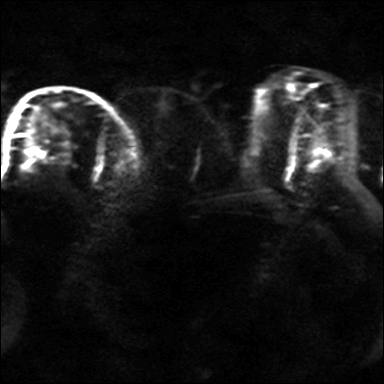
Breast MRI, one axial slice. Slice 20 of 36 in the series (ordered by position). Diffusion-weighted series; image 2 of 4 stored at this slice position (different b-values; order by instance number). 3 T. 4 mm slice thickness. 384 × 384 image matrix, field of view 320 × 320 mm. Female patient.
Structures marked on this image (manually delineated by an expert):
- tumour on diffusion-weighted imaging: bounding box [x1, y1, x2, y2] px = [23, 129, 73, 153]